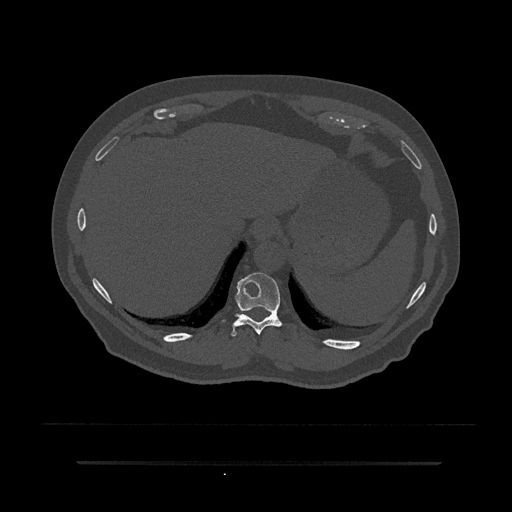
CT including the spine, one axial slice; slice 323 of 797 in the series (ordered by position); 120 kVp; bone window (W 1800 / L 400 HU); 512 × 512 image matrix, field of view 464 × 464 mm. Patient: male, 59 years. From the clinical record (not read from this slice): primary cancer: bile ducts.
Annotated regions visible in this slice (semi-automatically segmented with operator editing):
- T10 vertebra: bounding box (x1, y1, x2, y2) in pixels: (222, 273, 283, 337)